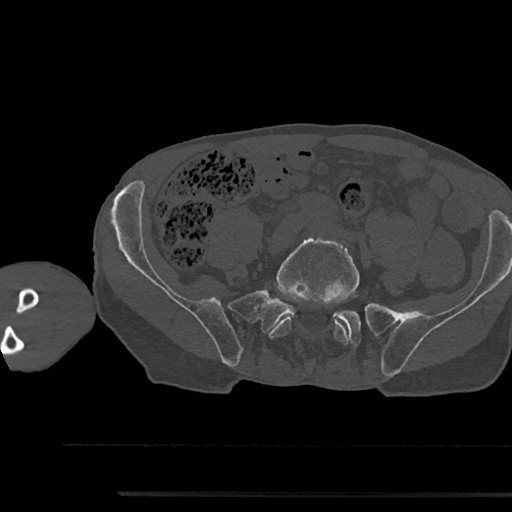
CT including the spine, one axial slice. Slice 324 of 797 in the series (ordered by position). Bone window (W 1800 / L 400 HU). 0.5 mm slice thickness. 512 × 512 image matrix, field of view 367 × 367 mm. Male patient, age 79 years. From the clinical record (not read from this slice): primary cancer: prostate.
Outlined on this slice (semi-automatically segmented with operator editing):
- L5 vertebra: bounding box [x1, y1, x2, y2] px = [268, 236, 359, 345]